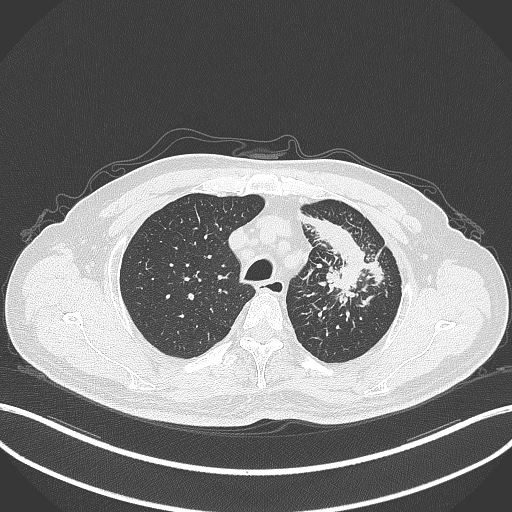
Chest CT, one axial slice. 120 kVp. Lung window (W 1500 / L -600 HU). 1 mm slice thickness. 512 × 512 image matrix, field of view 400 × 400 mm. Patient: male, 69 years. From the clinical record (not read from this slice): clinical TNM (as recorded): T2a N2 M0.
Structures marked on this image (rectangle marked by the reading radiologist):
- lung tumour (recorded histology: adenocarcinoma): bounding box <304,211,388,304> (left, top, right, bottom; pixels)